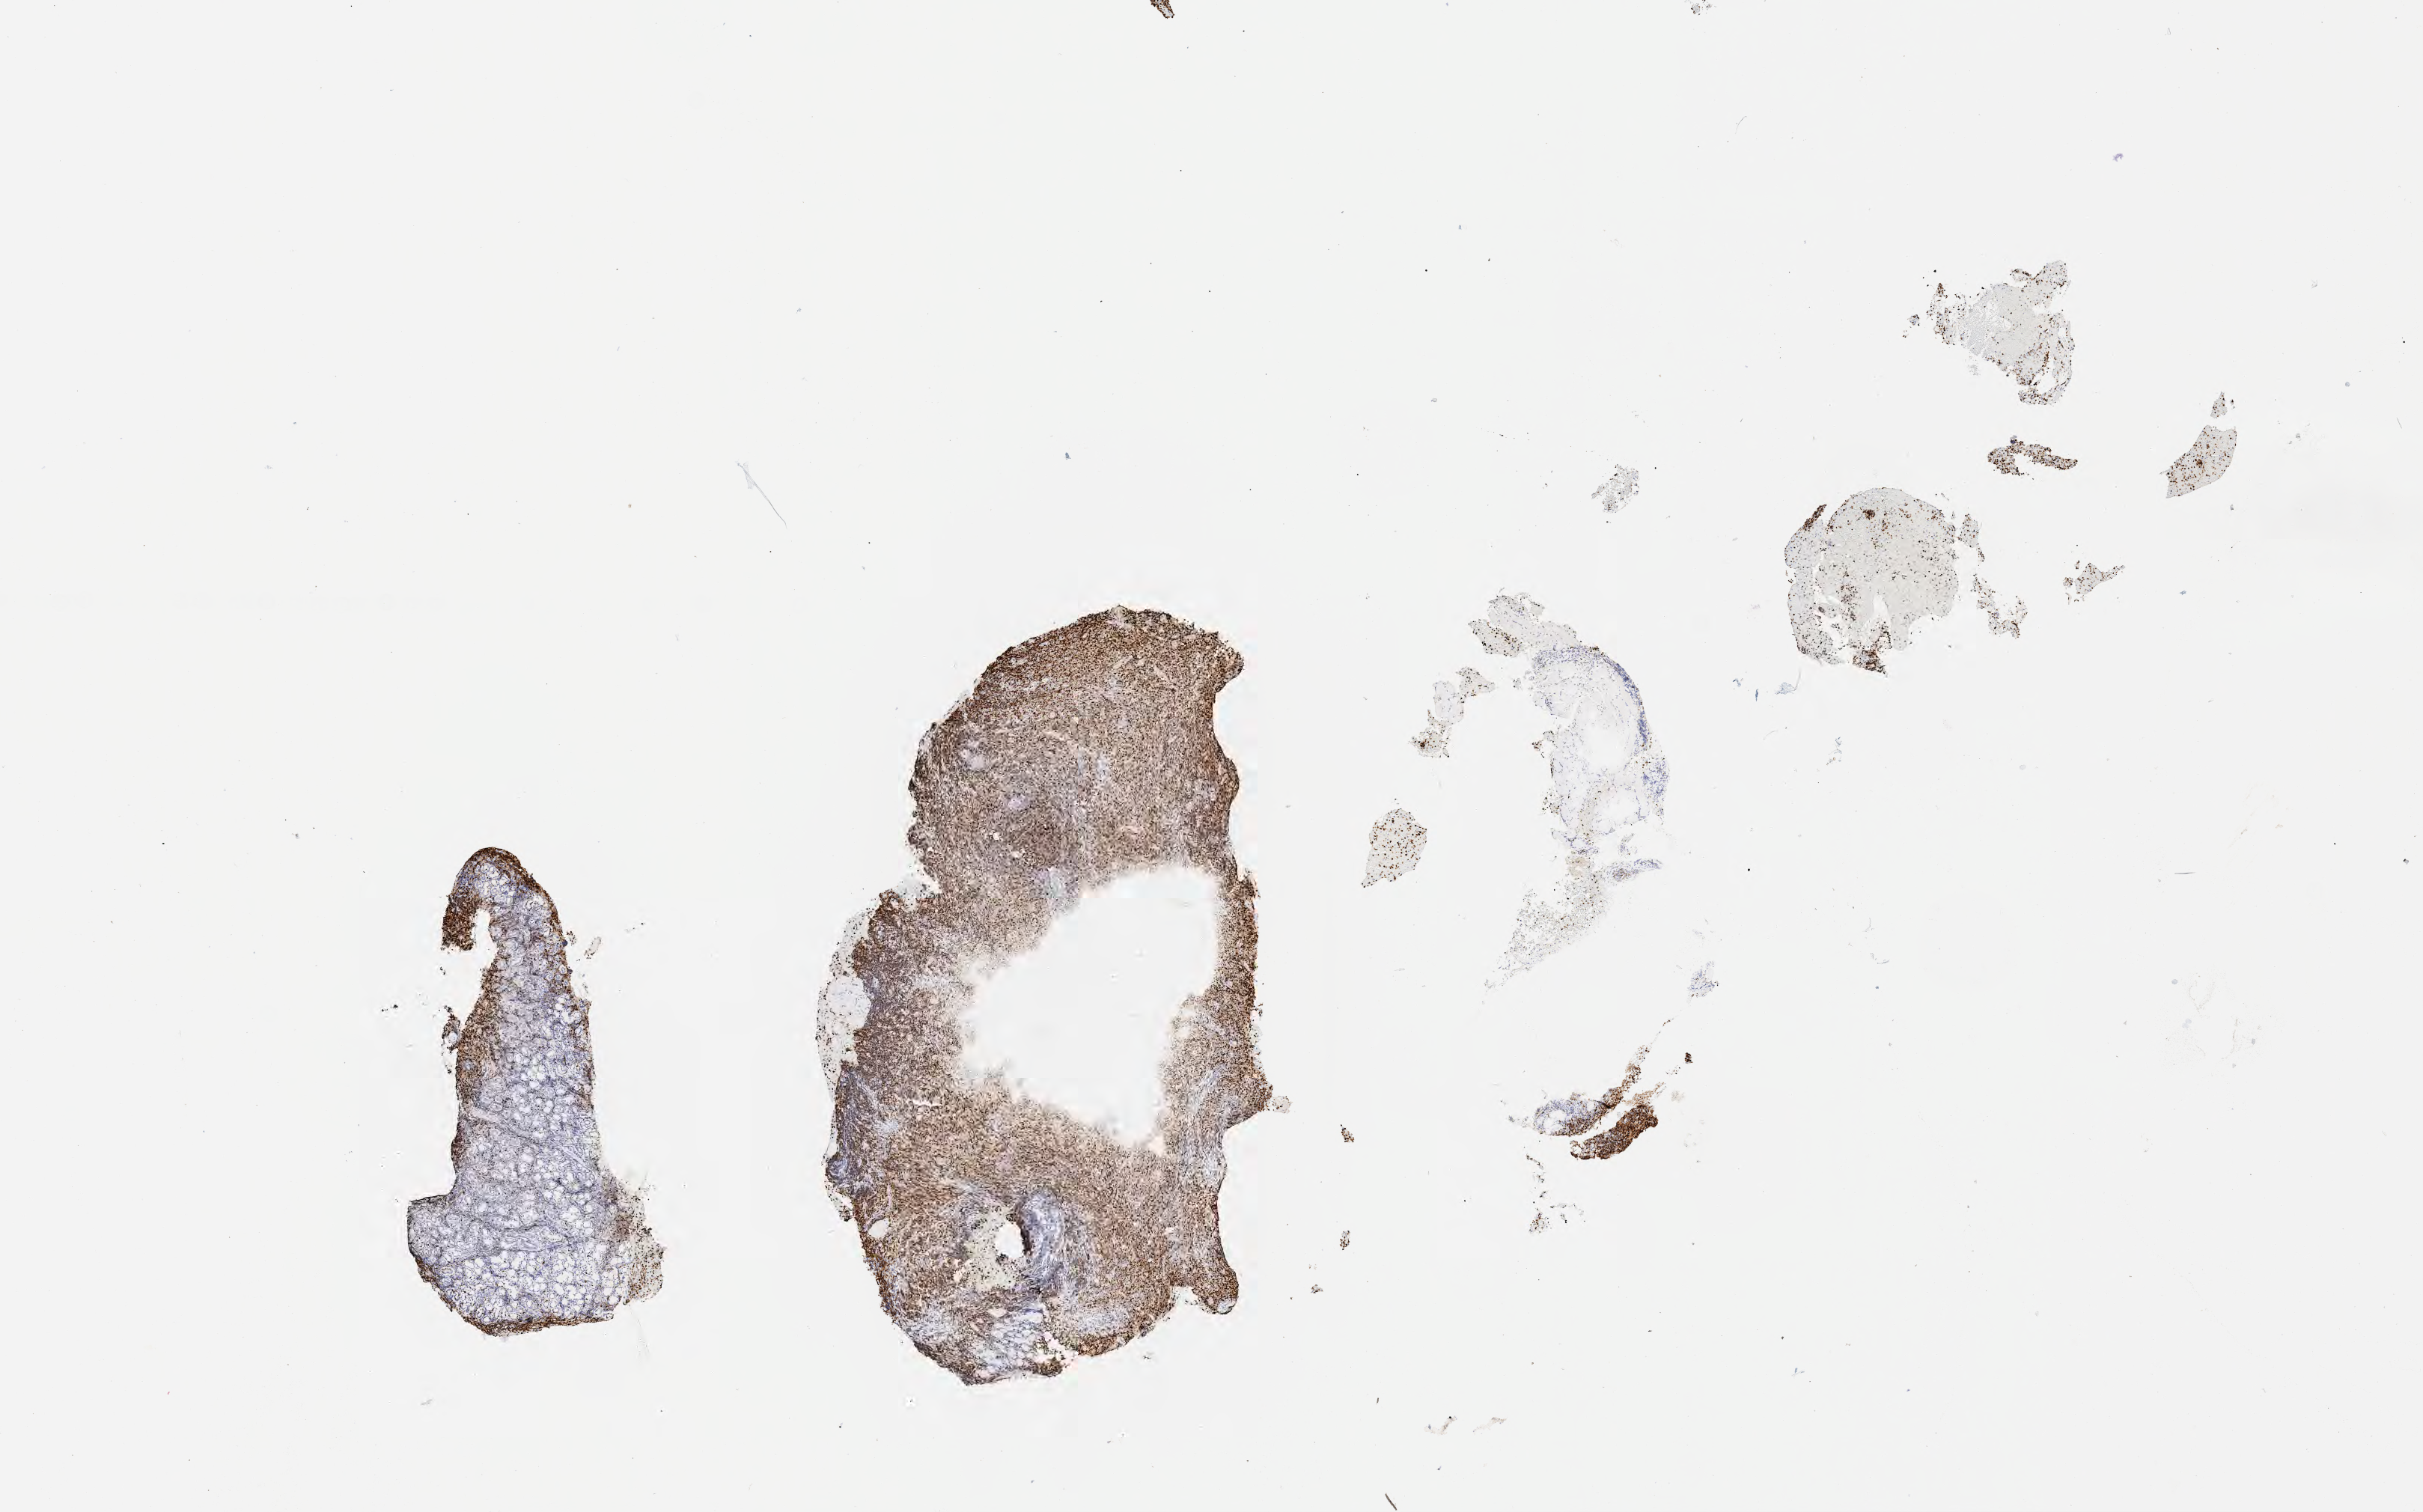
IHC for Ki-67, whole-slide image — whole scanned area (about 13.1 x 8.2 mm) shown as a low-resolution overview. Tumor tissue. Patient: male, age 53 years.
Histologic diagnosis: Diffuse large B-cell lymphoma, NOS.